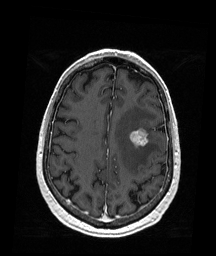
Brain MRI from a brain-tumour surgery series, one axial slice. Slice 63 of 176 in the series (ordered by position). T1-weighted post-contrast. 1 mm slice thickness. 216 × 256 image matrix, field of view 211 × 250 mm. Case-level facts recorded for this patient, not image findings: histopathology: Metastatic Melanoma.
Outlined on this slice (outlined manually by an expert reader):
- tumour: bounding box (x1, y1, x2, y2) in pixels: (129, 129, 150, 147)